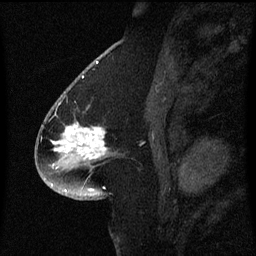
Breast MRI (dynamic contrast-enhanced), one sagittal slice. Position 31 of 60 along the scan axis. Dynamic contrast-enhanced series, image 2 of 3 at this slice position (ordered by acquisition). 1.5 T. TE 4.2 ms, TR 8.4 ms. 256 × 256 image matrix, field of view 200 × 200 mm. Female patient, age 54 years. Case-level facts recorded for this patient, not image findings: setting: breast cancer imaged before/during neoadjuvant chemotherapy; receptor status: HR-positive, HER2-negative.
Annotated regions visible in this slice (semi-automatically segmented with operator editing):
- analysis volume of interest (the breast-tissue region the enhancement analysis was run in; not a lesion): box from (x=46, y=102) to (x=112, y=171) px
- tumour enhancement mask (voxels above the 70 % enhancement threshold inside the analysis volume of interest): (x=54, y=126)–(x=106, y=151)